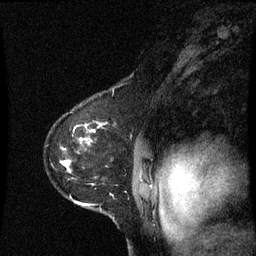
Breast MRI (dynamic contrast-enhanced), one sagittal slice; dynamic contrast-enhanced series, image 2 of 3 at this slice position (ordered by acquisition); 1.5 T; TE 4.2 ms, TR 8.9 ms; 2 mm slice thickness; 256 × 256 image matrix. Female patient, age 53 years. From the clinical record (not read from this slice): setting: breast cancer imaged before/during neoadjuvant chemotherapy; receptor status: HR-positive, HER2-negative.
Outlined on this slice (semi-automatic segmentation, software-assisted and operator-edited):
- analysis volume of interest (the breast-tissue region the enhancement analysis was run in; not a lesion): bounding box [x1, y1, x2, y2] px = [48, 112, 145, 221]
- tumour enhancement mask (voxels above the 70 % enhancement threshold inside the analysis volume of interest): [62, 130, 95, 207]